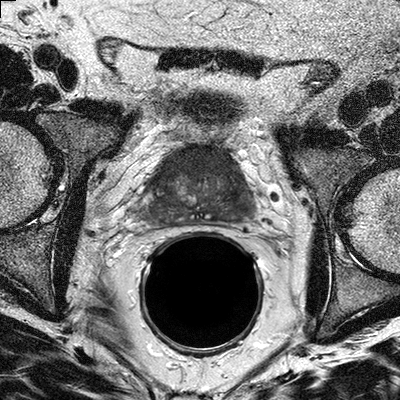
Prostate MRI examination; 3 images, each a single mid-volume slice chosen by position (not for content). Treatment context recorded for this patient: No surgery.
Image 1: axial T2-weighted image, slice 17 of 32.
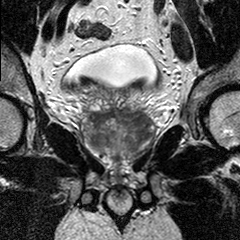
Image 2: T2-weighted coronal slice, series "T2W_TSE_COR", slice 16 of 30, 3 mm slice thickness.
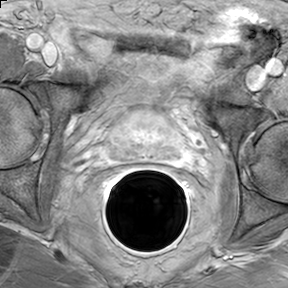
Image 3: axial dynamic contrast-enhanced (DCE) T1-weighted image, series "AX BLISS_GAD_8", slice 17 of 32, dynamic phase 5 of 8.
Radiologist's MRI report for this examination:
Zonal anatomy is preserved. Maximal transverse diameter 5.1 cm;
maximal AP diameter 3.1 cm ; maximal CC diameter 3.5 cm. Estimated total gland volume of 29 cc. The entire prostate including central gland as well as left and right peripheral zone show diffuse T2 hyperintense signal alterations suggestive for diffuse chronic prostatitis. The central gland shows mild BPH. In the left posterior lateral apex, (5-6 o'clock) the left posterior lateral peripheral zone (4-5 o'clock) of the mid 3rd of the gland and left lateral peripheral zone (3 o'clock) of the base as well as the anterior gland in proximity to the fibromuscular band (10-2 o'clock) show more geographic hypo intensities on the T2 weighted images suspicious for malignancy. No evidence of extra prostatic extension; no evidence of involvement of the neuro vascular bundle seen on either side. The seminal vesicles are unremarkable. No suspicious the largest obturator or iliac lymph nodes on either side. IMPRESSION:Diffuse chronic prostatitis involving the entire prostate. Mild BPH. Most suspicious areas for malignancy are seen in the anterior gland in proximity to the fibromuscular band between 10 and 2 o'clock, and in the left lateral and posterior lateral peripheral zone. (as detailed above. Unremarkable neurovascular bundles and seminal vesicles ; no pelvic lymphadenopathy.

Prostate biopsy pathology (as recorded):
PROSTATE CORE NEEDLE BIOPSIES: 1. RIGHT PZ:PROSTATIC TISSUE WITH CHRONIC INFLAMMATION. NO TUMOR IDENTIFIED. 2. RIGHT PZ/TZ:PROSTATIC TISSUE WITH ACUTE AND CHRONIC INFLAMMATION. NO TUMOR IDENTIFIED. 3. RIGHT APEX: PROSTATIC TISSUE WITH CHRONIC INFLAMMATION. NO TUMOR IDENTIFIED. 4. LEFT PZ: FOCAL HIGH GRADE PIN. 5. LEFT PZ/TZ: PROSTATIC TISSUE. NO TUMOR IDENTIFIED. 6. LEFT APEX: PROSTATIC TISSUE. NO TUMOR IDENTIFIED.